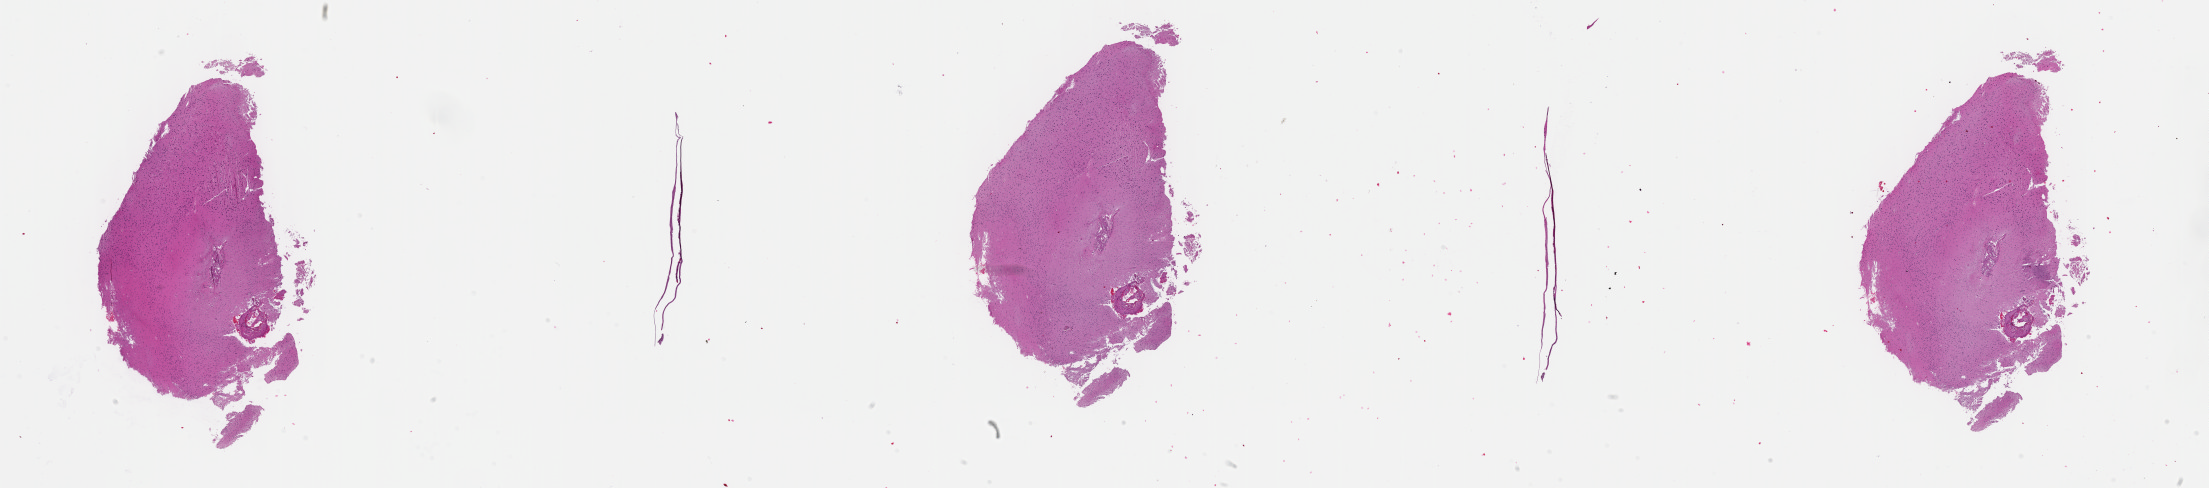
H&E-stained whole-slide image — whole scanned area (about 35.7 x 7.9 mm, slide scanned at 40x) shown as a low-resolution overview. Formalin-fixed paraffin-embedded (FFPE) diagnostic section. Sample: primary tumour, brain. Female patient; age at initial diagnosis 74 years. Histologic grade: G2 (moderately differentiated).
Histologic diagnosis: Mixed glioma.